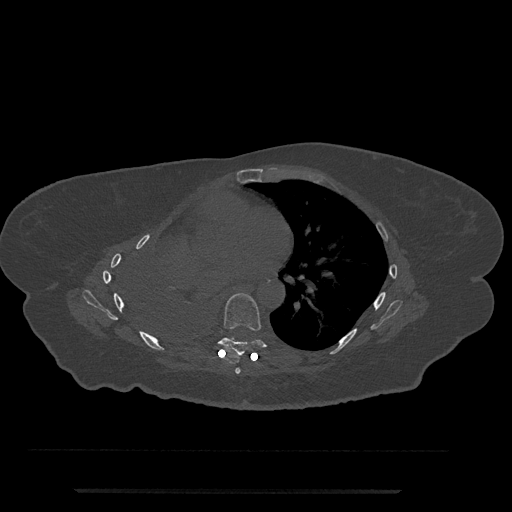
CT including the spine, one axial slice. Position 440 of 797 along the scan axis. Reconstruction kernel Br40s/3. Bone window (W 1800 / L 400 HU). 0.5 mm slice thickness. 512 × 512 image matrix. Patient: female, 51 years. Case-level facts recorded for this patient, not image findings: primary cancer: neuro.
Outlined on this slice (semi-automatically segmented with operator editing):
- T6 vertebra: bounding box <235,367,241,374> (left, top, right, bottom; pixels)
- T7 vertebra: <207,293,278,358>